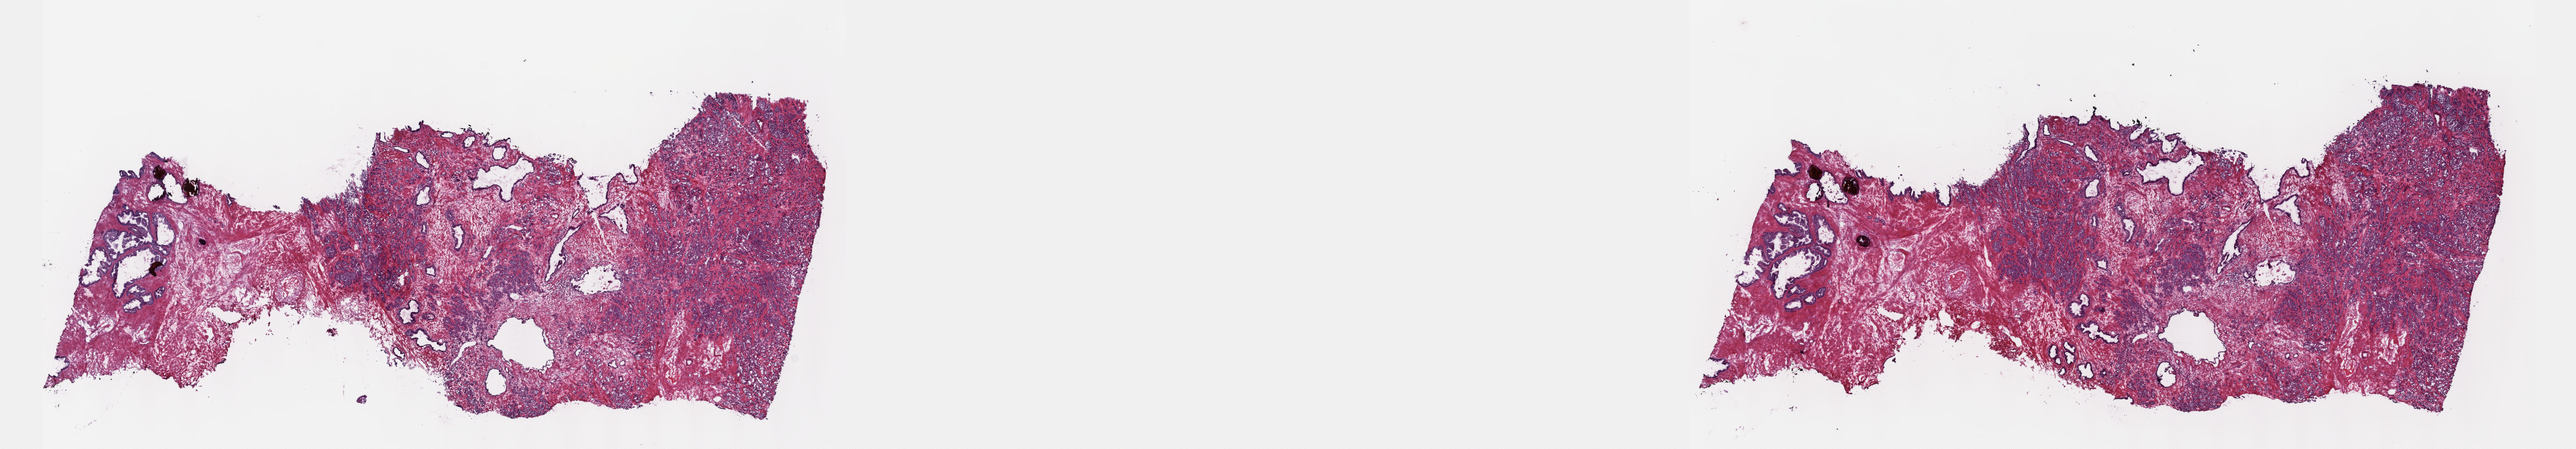
Whole-slide histology image, H&E, a low-resolution overview of the entire scanned area, about 30.7 x 5.3 mm (acquisition: 40x scan); frozen section from the top of the tissue portion; primary tumour sample from the prostate. Male patient; age at initial diagnosis 70 years.
Diagnosis: Adenocarcinoma, NOS.